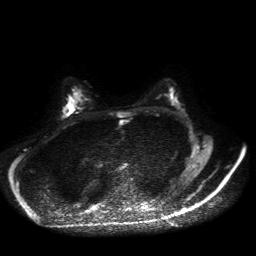
Breast MRI, one axial slice; slice 25 of 50 in the series (ordered by position); diffusion-weighted series; image 2 of 4 stored at this slice position (different b-values; order by instance number); 1.5 T; 4 mm slice thickness; 256 × 256 image matrix, field of view 360 × 360 mm. Female patient.
Outlined on this slice (outlined manually by an expert reader):
- tumour on diffusion-weighted imaging: bounding box <63,104,73,115> (left, top, right, bottom; pixels)